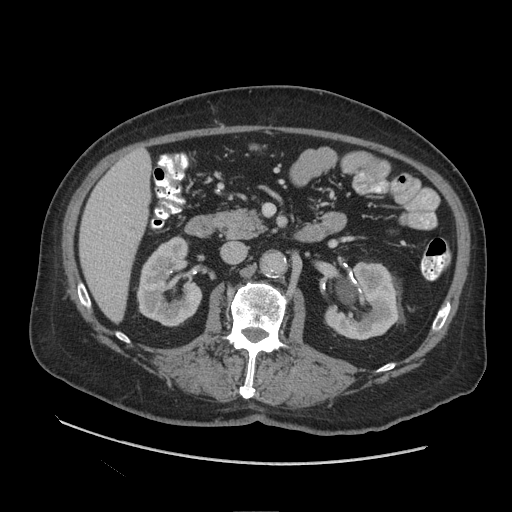
Contrast-enhanced abdominal CT (liver protocol), one axial slice. Position 37 of 109 along the scan axis. Reconstruction kernel STANDARD. Soft-tissue window (W 400 / L 40 HU). 2.5 mm slice thickness. 512 × 512 image matrix, field of view 420 × 420 mm. Case-level facts recorded for this patient, not image findings: diagnosis: hepatocellular carcinoma (patient treated with transarterial chemoembolisation; whether this scan precedes or follows treatment is not stated here); TNM stage (as recorded): Stage-I; Child-Pugh class: A; tumour nodularity: uninodular.
Structures marked on this image (semi-automatic segmentation, software-assisted and operator-edited):
- liver parenchyma outside the tumour (the mass and vessels are separate outlines, so this box may not span the whole liver): bounding box (x1, y1, x2, y2) in pixels: (80, 150, 150, 320)
- liver vessels: (123, 204, 126, 207)